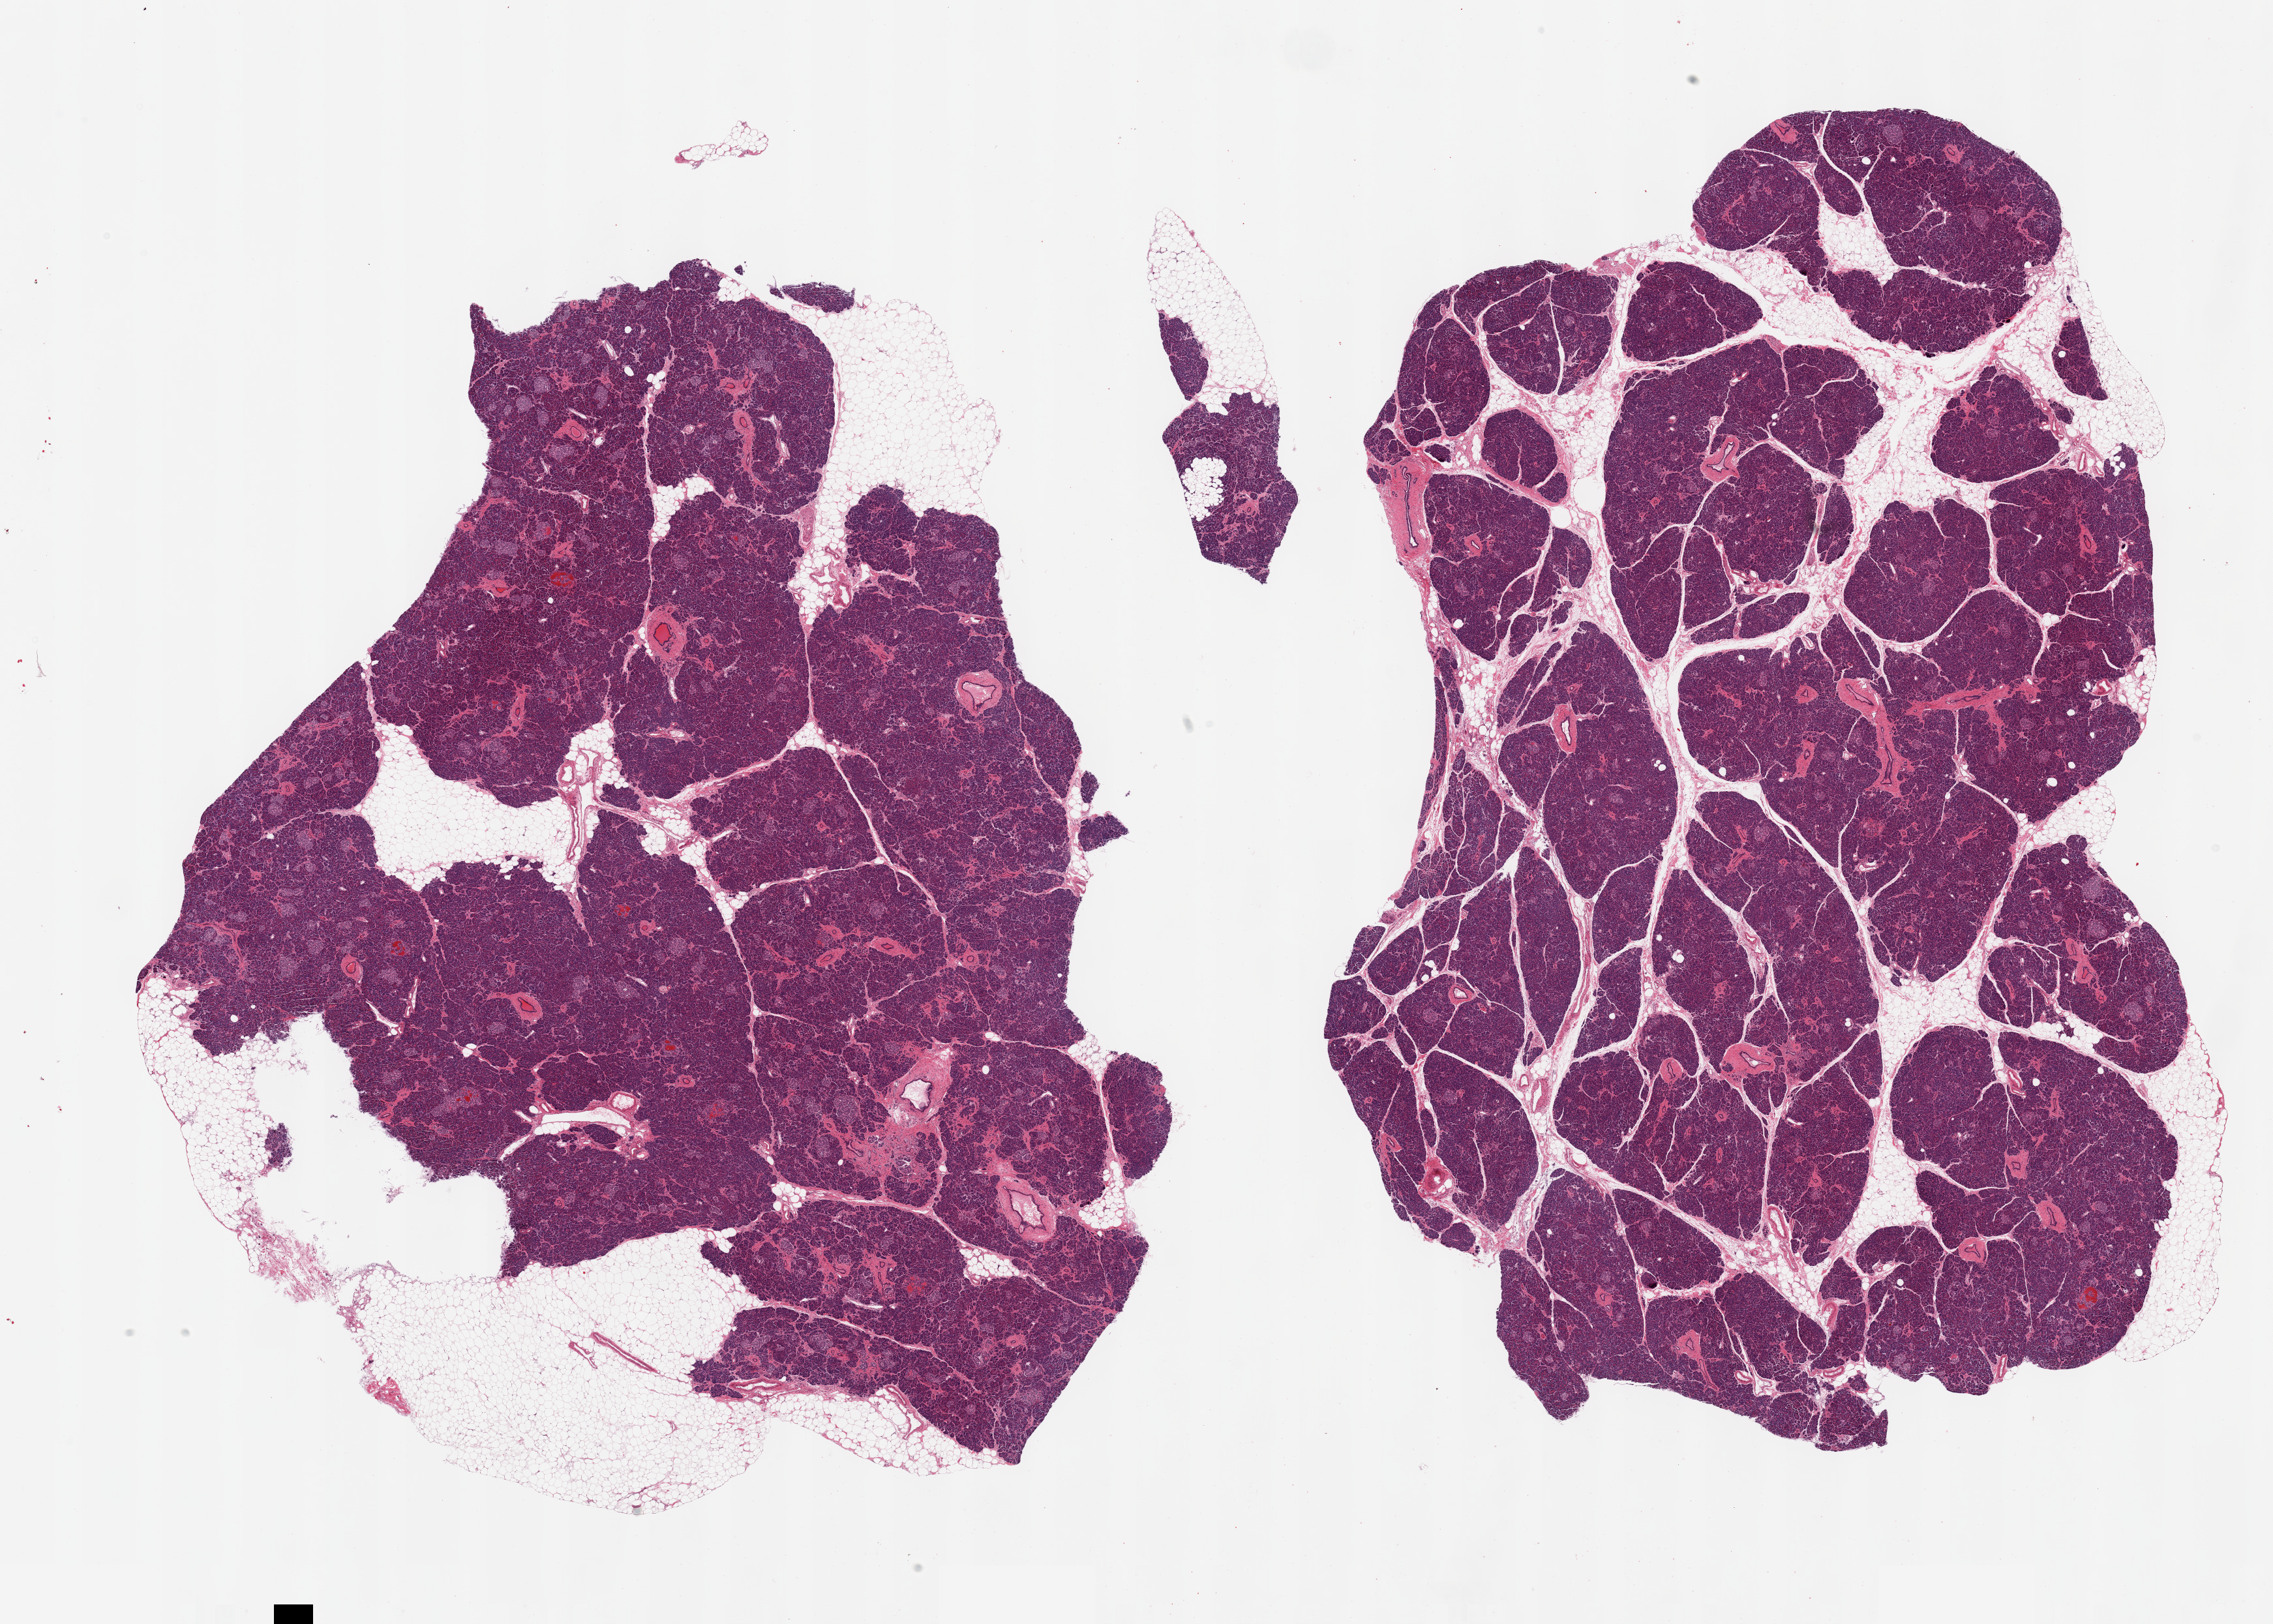
Haematoxylin and eosin whole-slide image — shown as a low-resolution overview of the whole scanned area (about 27.6 x 19.7 mm, slide scanned at 20x); PAXgene-fixed, paraffin-embedded tissue; target tissue: pancreas; donor tissue sample. Donor: male.
* review note (as recorded): 2 pieces, exceptionally well-preserved, Islets abundant, well visualized